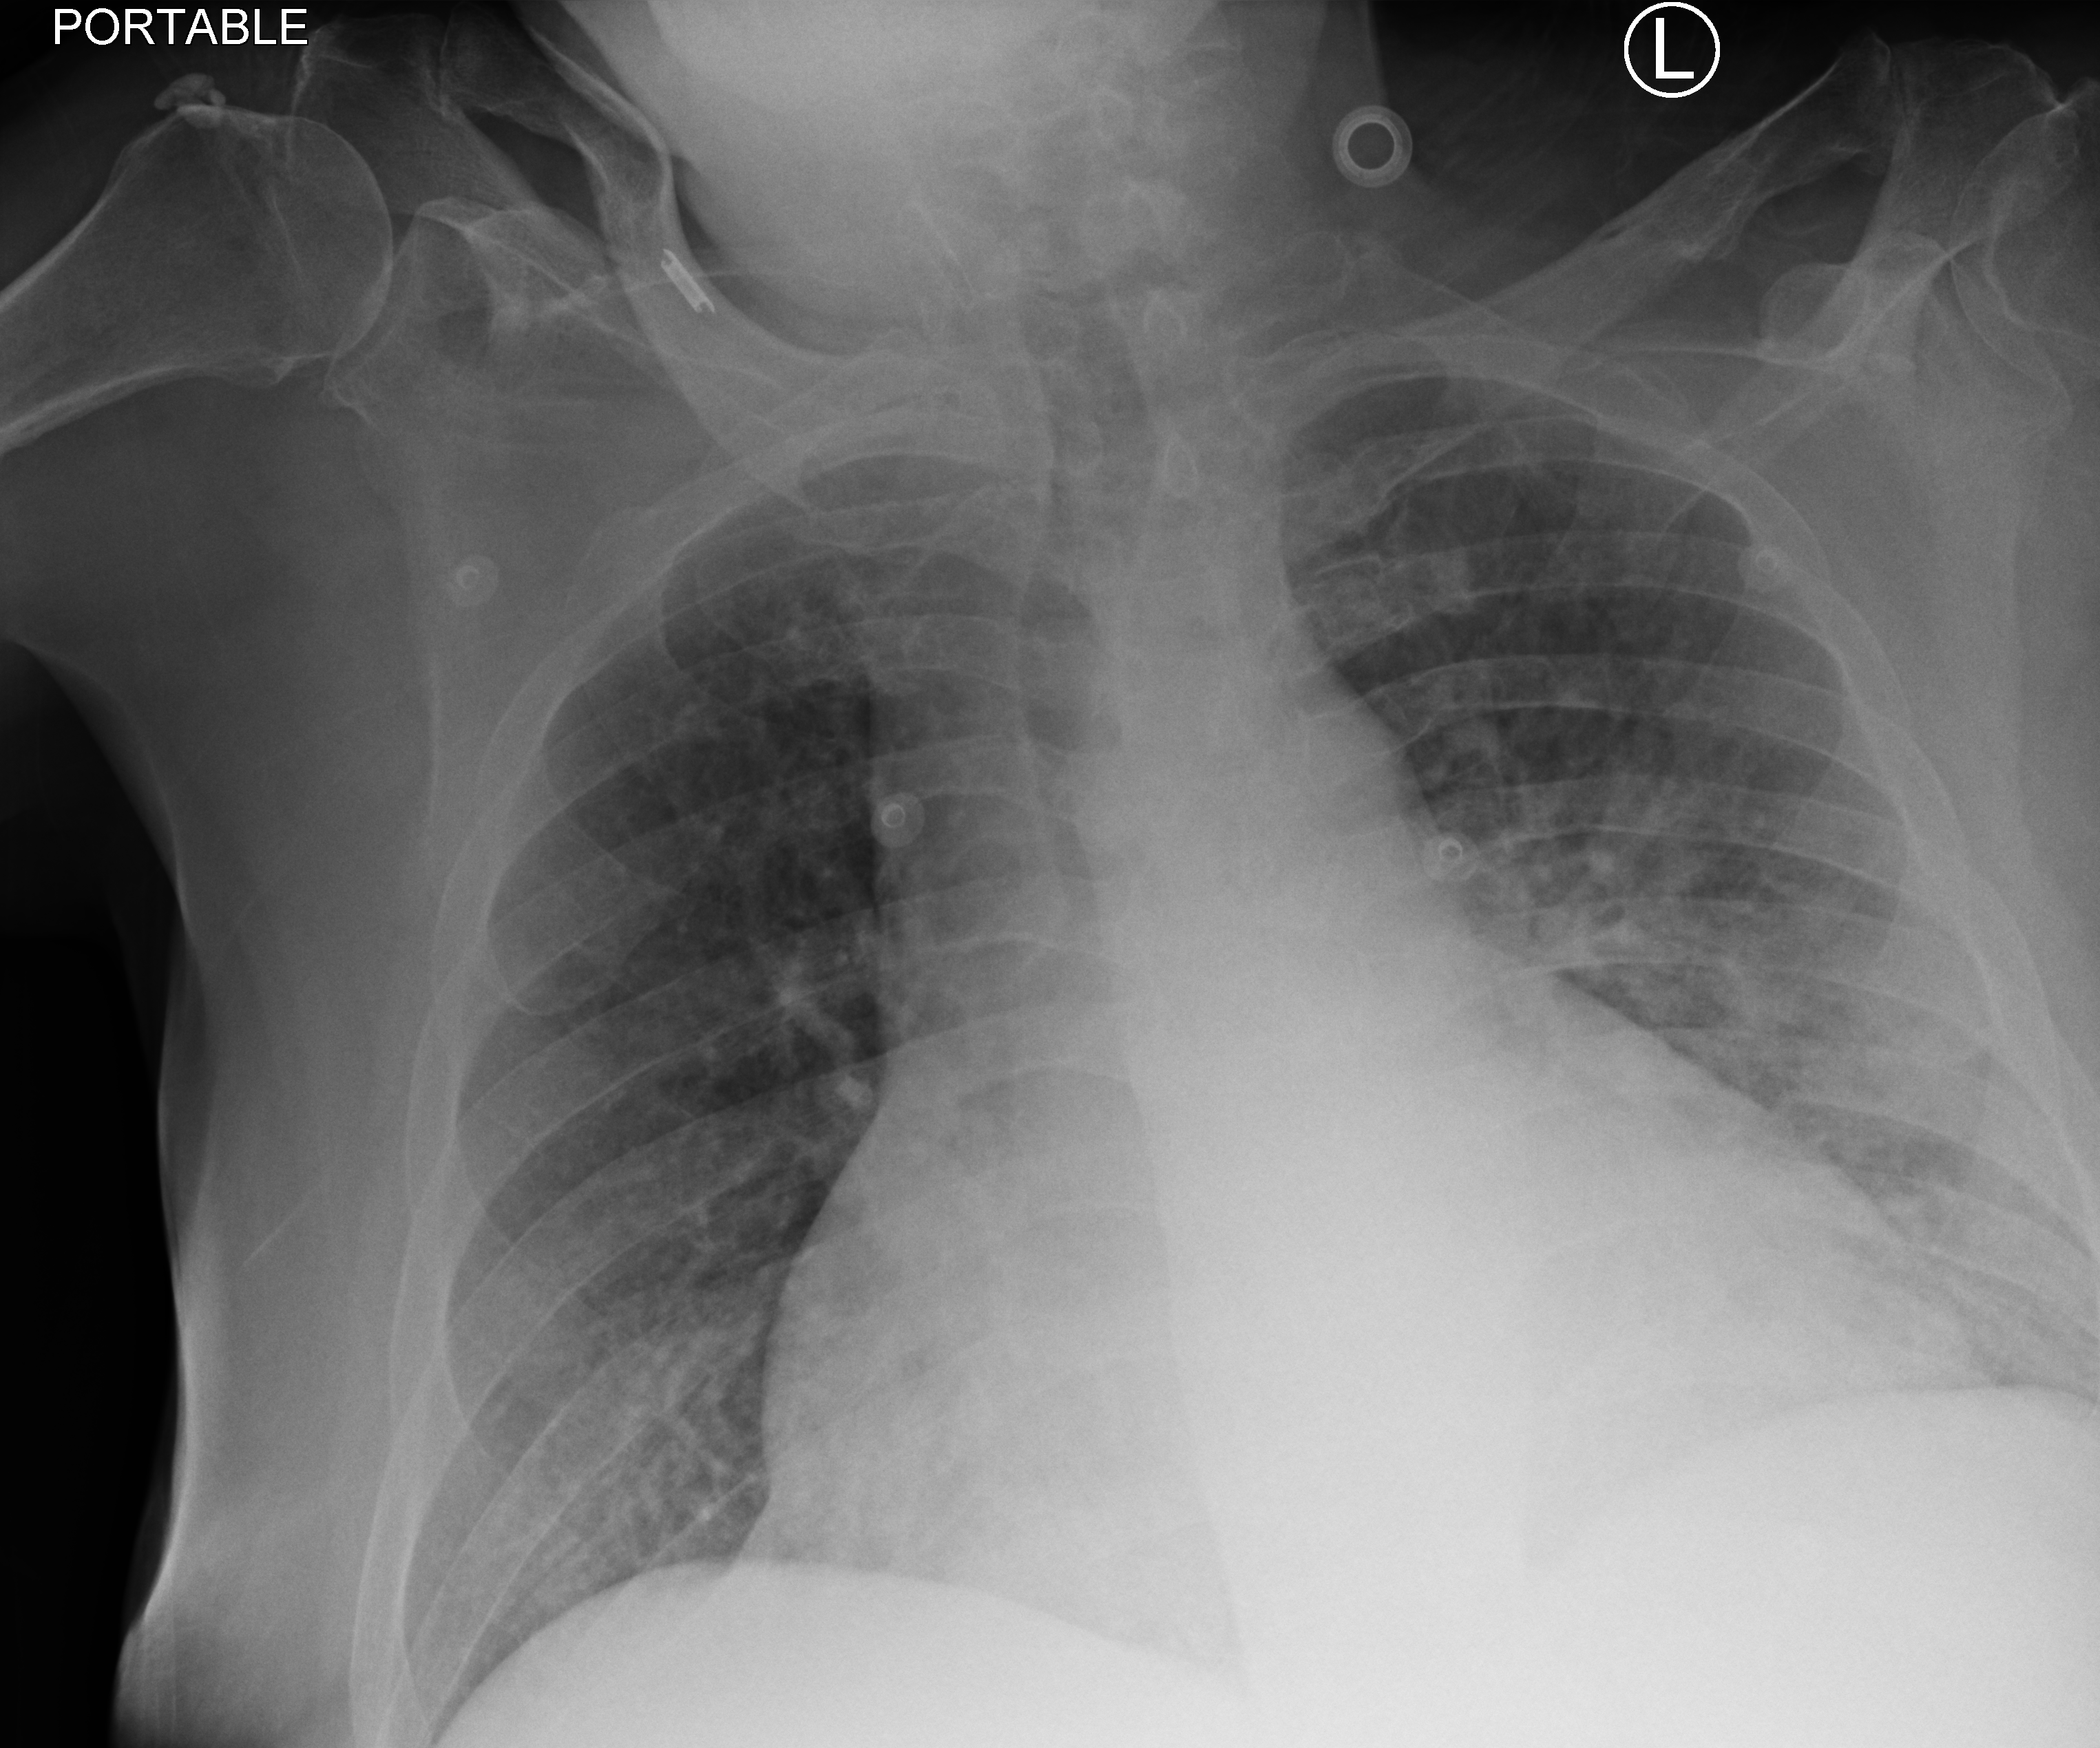
Portable chest radiograph. Male patient hospitalised with COVID-19, age 18–59 years.
From the hospital-stay record, not from the radiograph (when in the stay this image was taken is not recorded):
- mechanically ventilated during this hospital stay: no